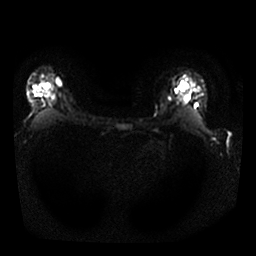
Breast MRI, one axial slice. Slice 21 of 25 in the series (ordered by position). Diffusion-weighted series; image 2 of 4 stored at this slice position (different b-values; order by instance number). 1.5 T. 256 × 256 image matrix. Female patient.
Outlined on this slice (manually delineated by an expert):
- tumour on diffusion-weighted imaging: box from (x=36, y=83) to (x=43, y=93) px